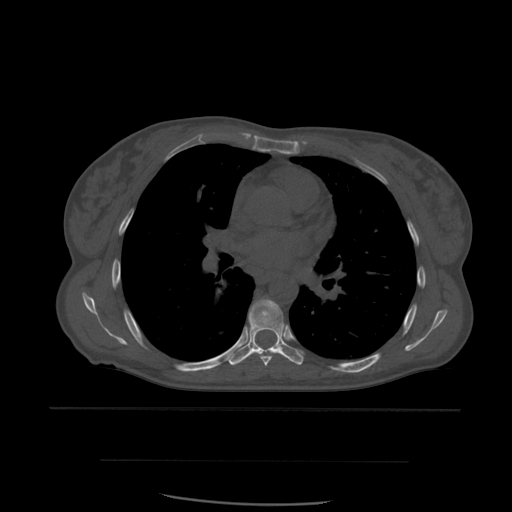
CT including the spine, one axial slice. Slice 381 of 574 in the series (ordered by position). Bone window (W 1800 / L 400 HU). 512 × 512 image matrix, field of view 392 × 392 mm. Patient age 48 years. From the clinical record (not read from this slice): primary cancer: lung.
Structures marked on this image (semi-automatic segmentation, software-assisted and operator-edited):
- T6 vertebra: bounding box [x1, y1, x2, y2] px = [258, 353, 276, 367]
- T7 vertebra: [230, 299, 304, 366]